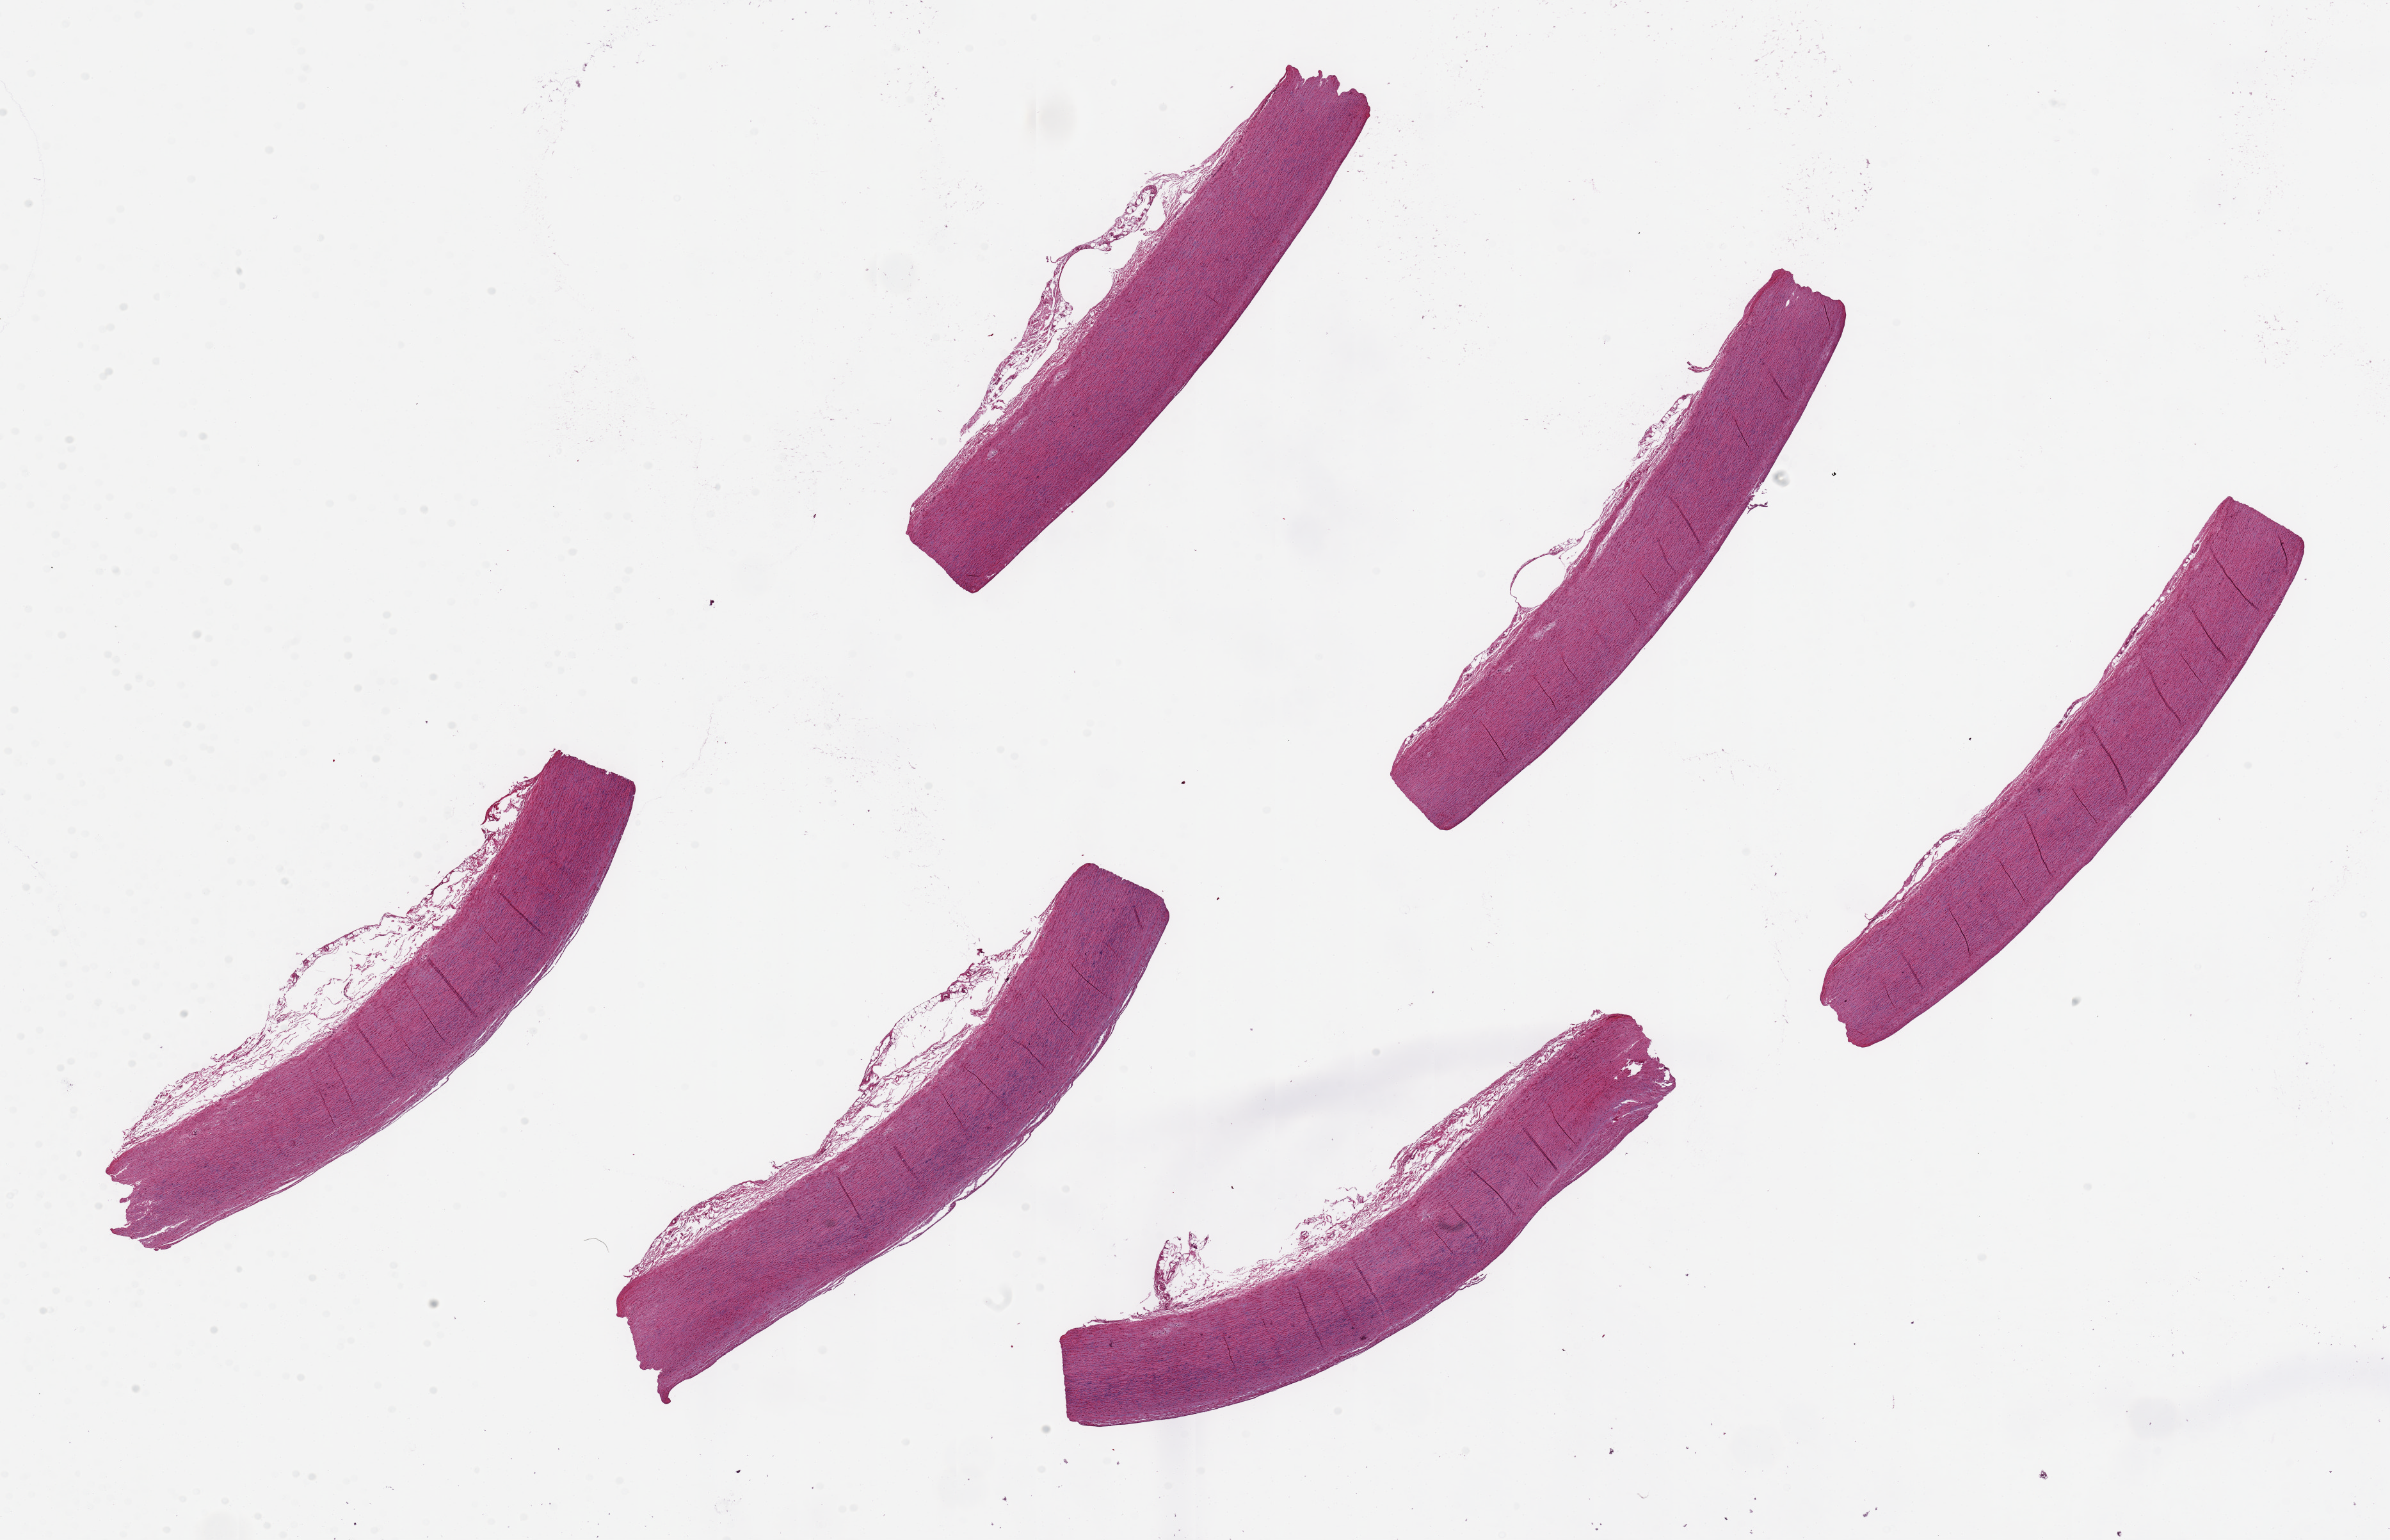
Digitized haematoxylin and eosin-stained section, brightfield — a low-resolution overview of the entire scanned area, about 29.5 x 19.0 mm. PAXgene-fixed, paraffin-embedded tissue. Target tissue: aorta. Donor tissue sample. Donor: female.
Pathologist's review note for this sample: 6 pieces up to 8x1.3 mm; clean adventitia.